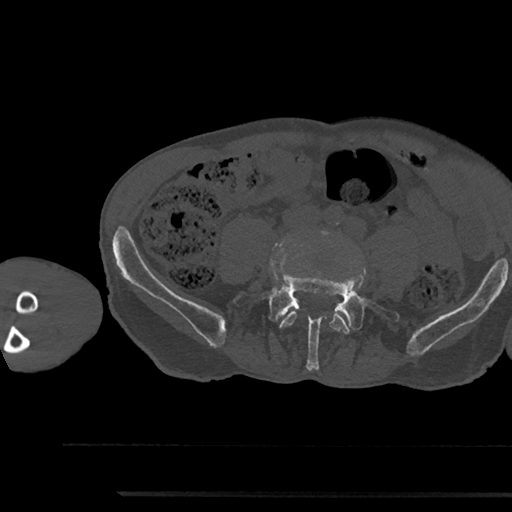
CT including the spine, one axial slice. Slice 370 of 797 in the series (ordered by position). Reconstruction kernel Br40s/3. 120 kVp. Bone window (W 1800 / L 400 HU). 512 × 512 image matrix, field of view 367 × 367 mm. Male patient, age 79 years. From the clinical record (not read from this slice): primary cancer: prostate.
Structures marked on this image (semi-automatic segmentation, software-assisted and operator-edited):
- L4 vertebra: bounding box (x1, y1, x2, y2) in pixels: (279, 242, 349, 334)
- L5 vertebra: (234, 264, 400, 370)